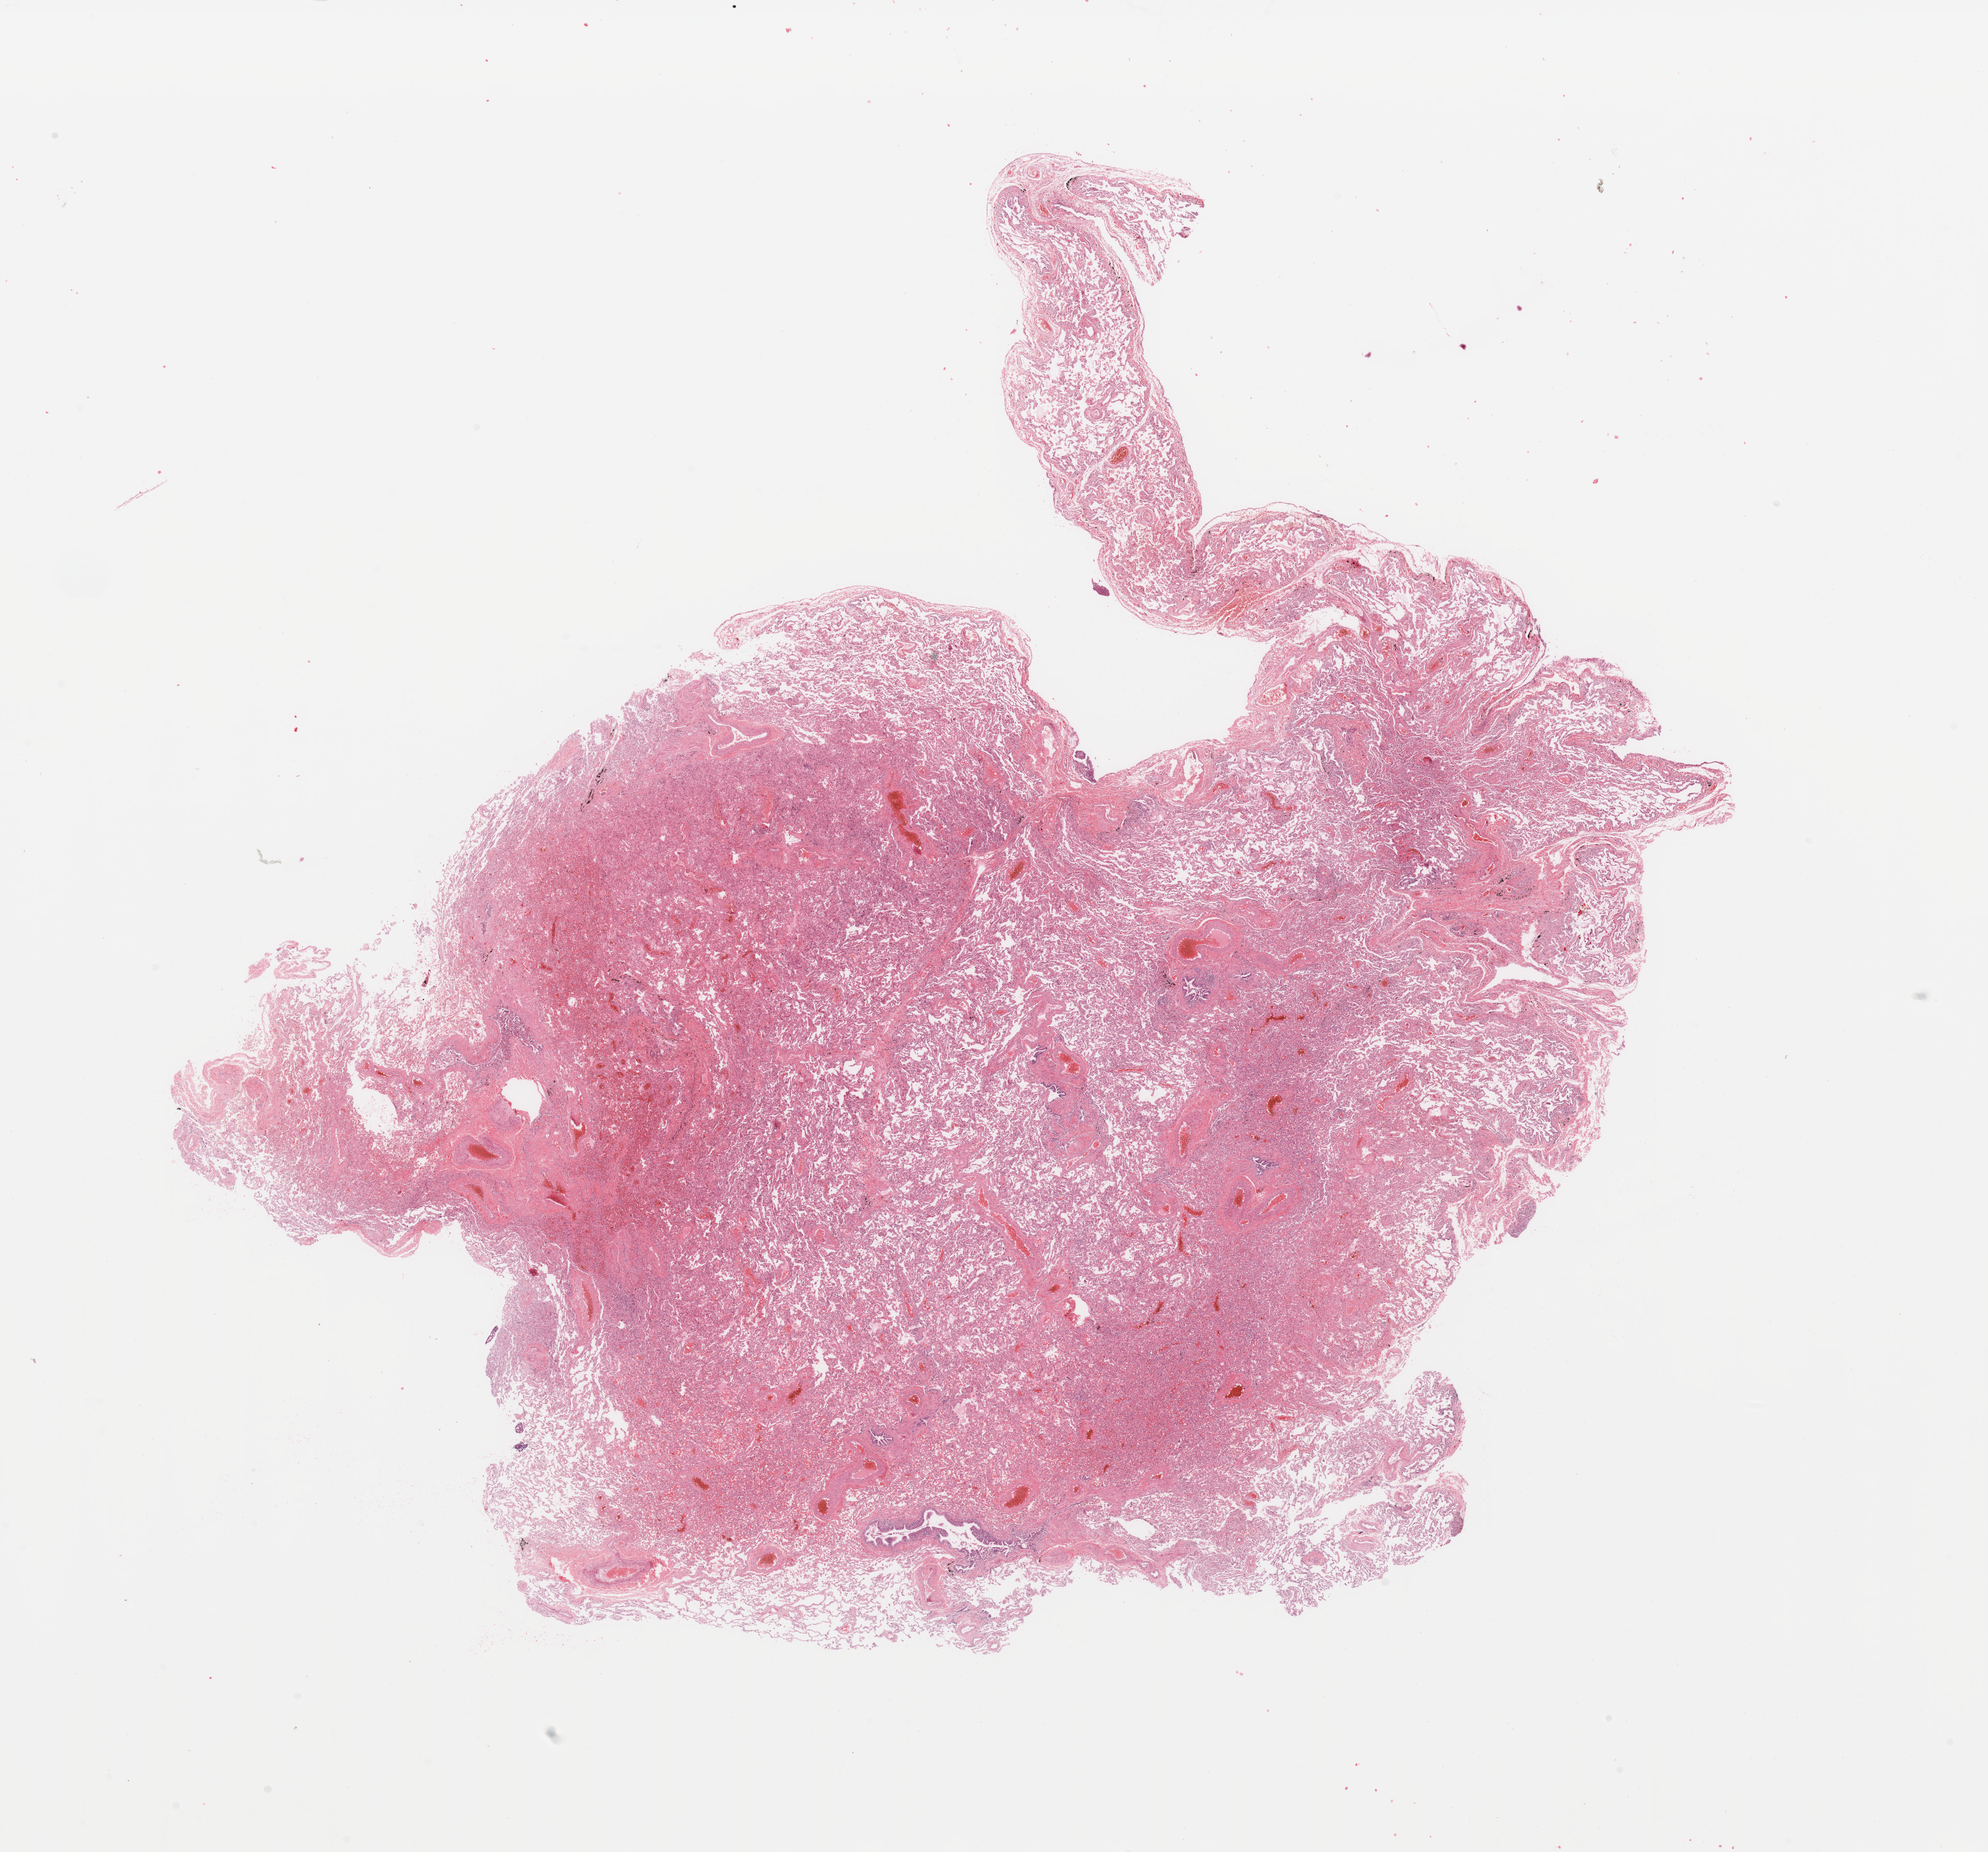
Whole-slide histology image, H&E-stained, low-resolution overview of the scanned area, about 23.6 x 22.0 mm (acquisition: 20x scan). Normal (non-tumour) tissue sample, sampled site: lung. Male, 58 y/o.
This section: normal (non-tumour) tissue from the same patient. Patient diagnosis: Adenocarcinoma, NOS.